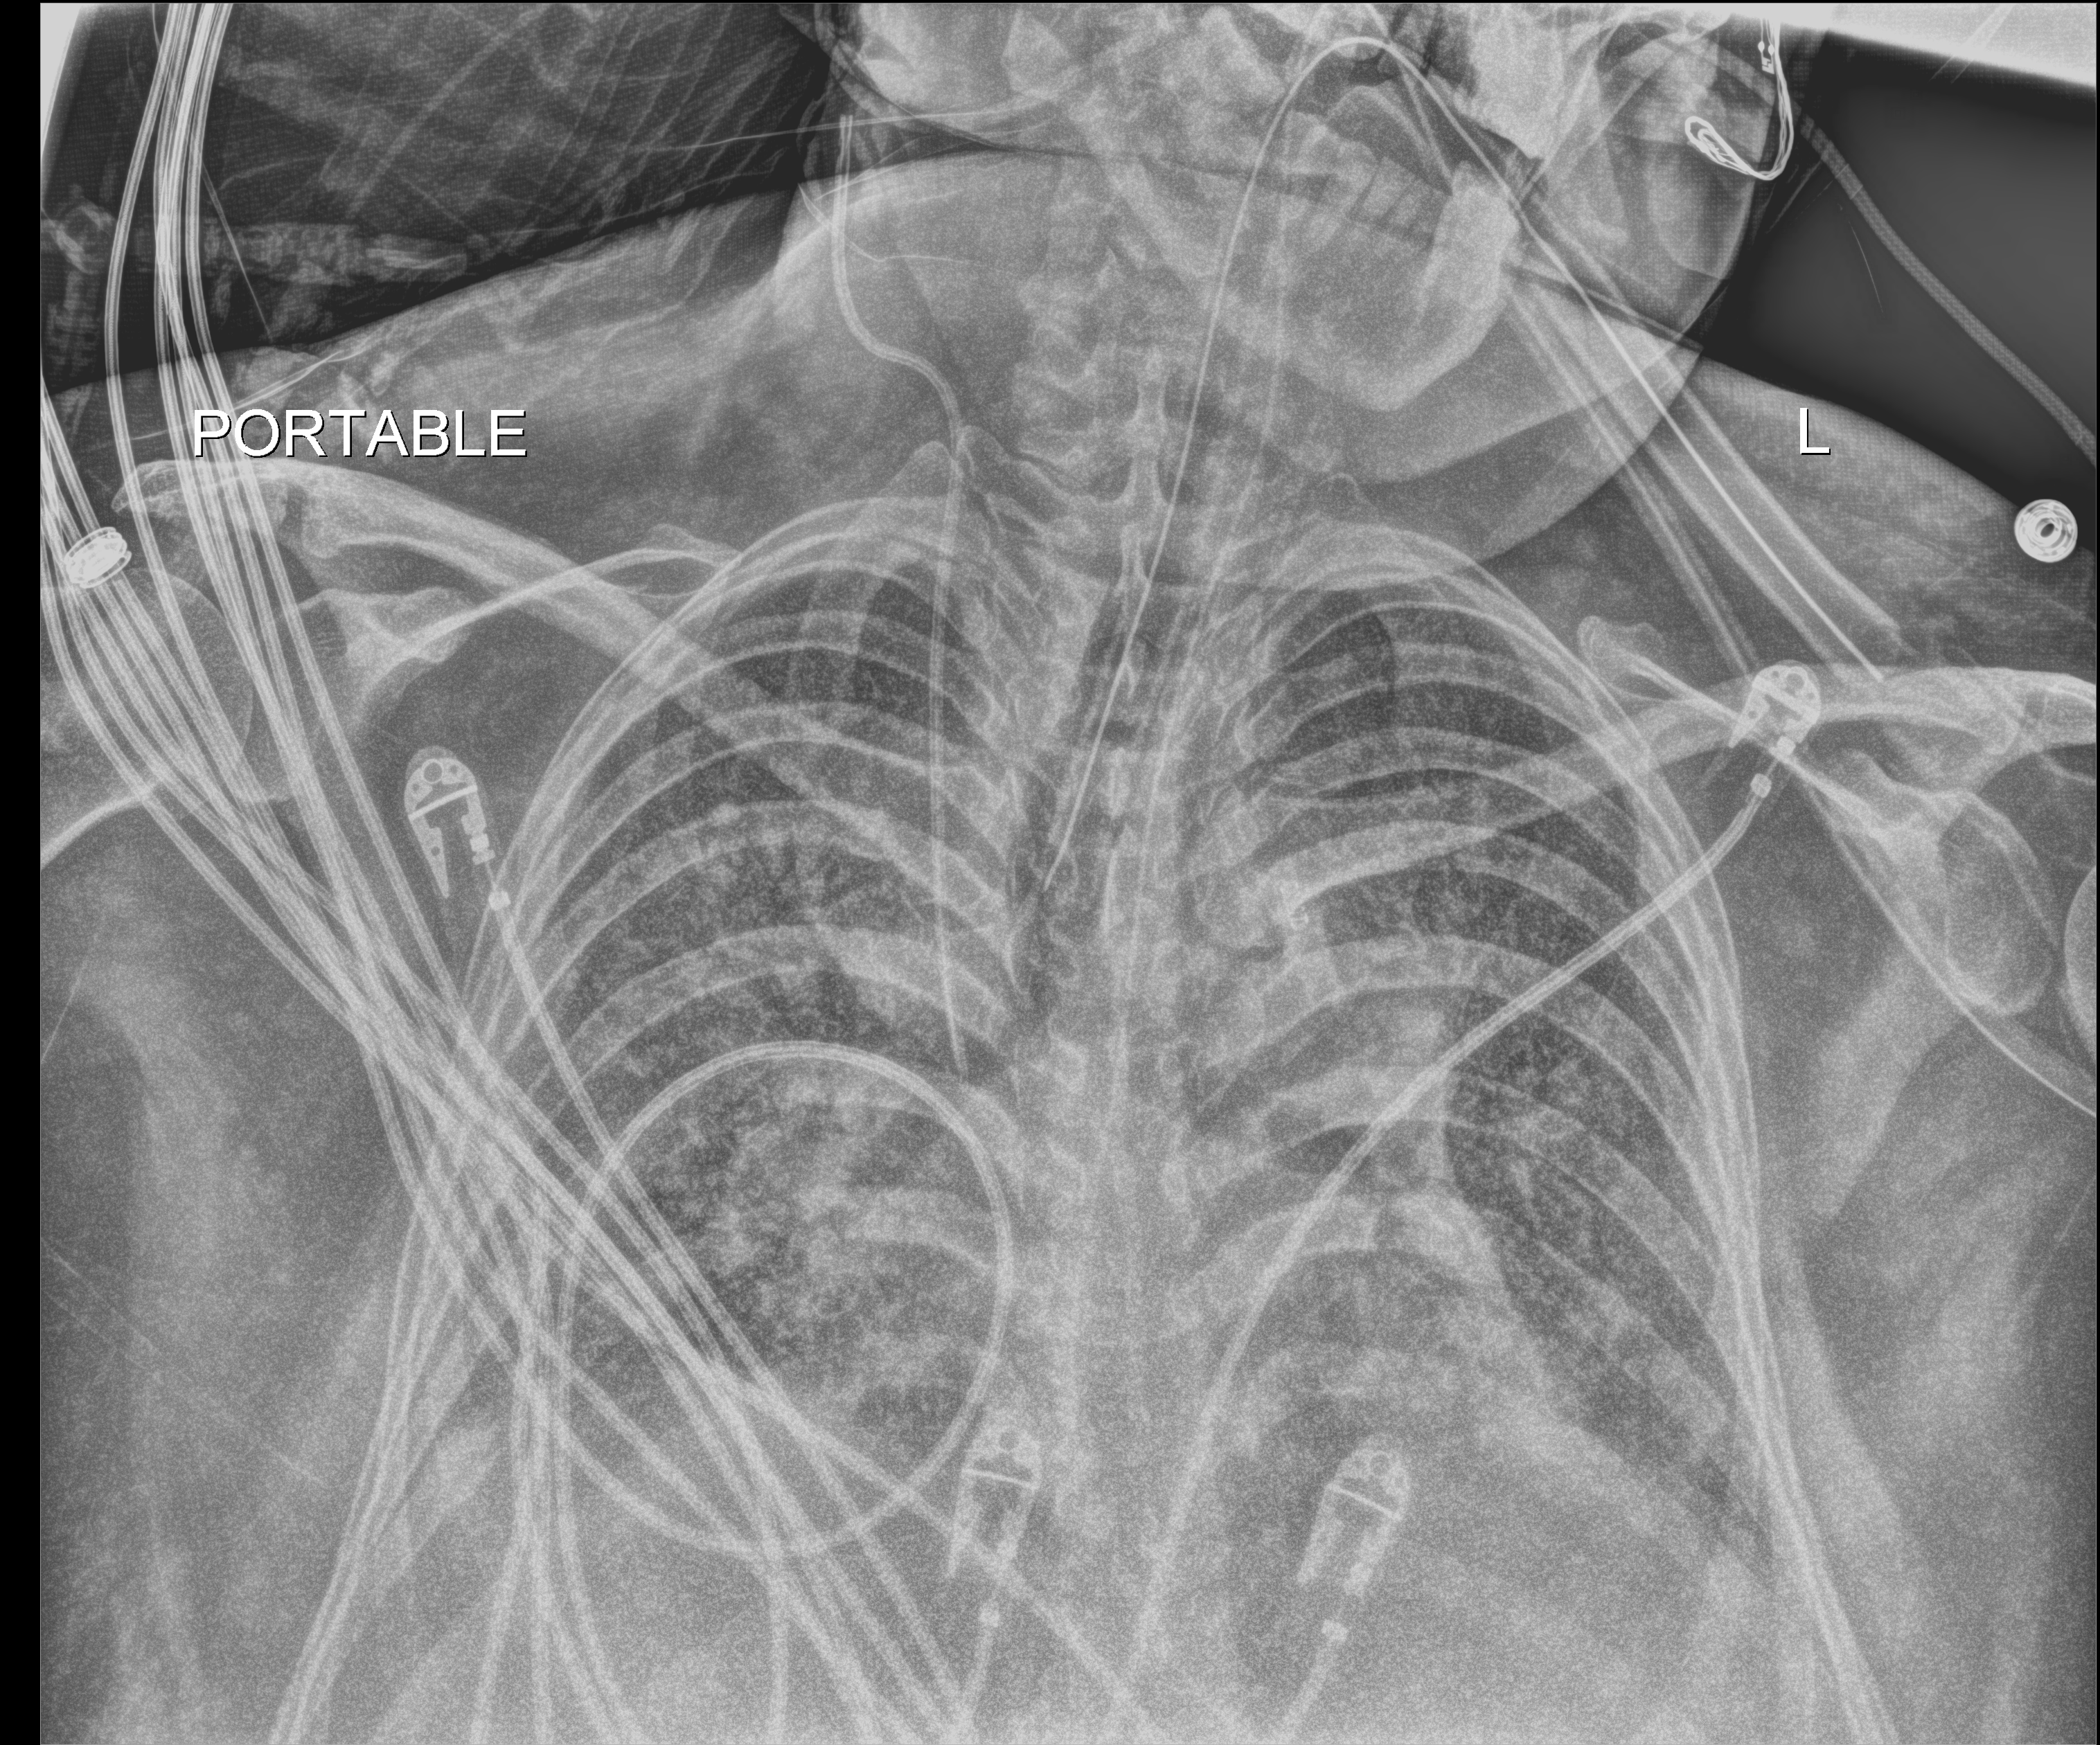
Portable chest radiograph; anteroposterior (AP) projection. Patient hospitalised with COVID-19, aged 18–59 years.
Hospital-stay facts (about this admission, not read from this image; timing relative to this image not recorded):
- chronic kidney disease (admission record): no
- mechanically ventilated during this hospital stay: yes
- admitted to intensive care during this hospital stay: yes